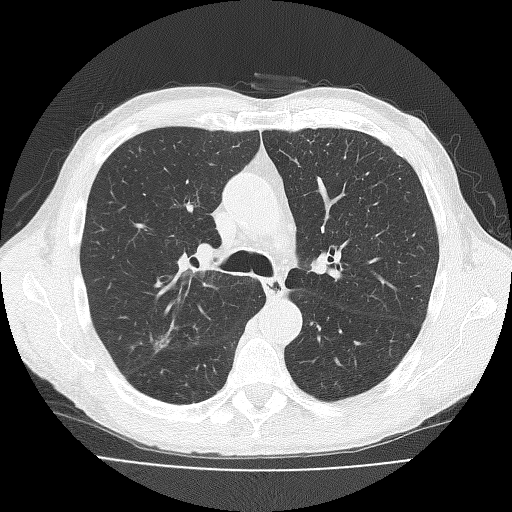
Chest CT (low-dose screening protocol), one axial image, third screening round (two years after baseline), lung window (W 1500 / L -600 HU), 2 mm slice thickness, 512 × 512 image matrix. Male, age 73 years at enrolment. Current smoker at enrolment.
Expert-annotated lung lesion, bounding box <138,315,195,378> (left, top, right, bottom; pixels). Reader record for this screening exam (exam-level; its link to the box is not recorded): non-calcified nodule or mass ≥4 mm, right upper lobe, 11 × 10 mm, spiculated (stellate) margins, soft tissue attenuation, pre-existing on the prior screen: no. Later outcome: lung cancer diagnosed 38 days after this screen — adenosquamous carcinoma, right upper lobe, well differentiated (G1), stage IA (AJCC 6th edition), 20 mm at pathology.